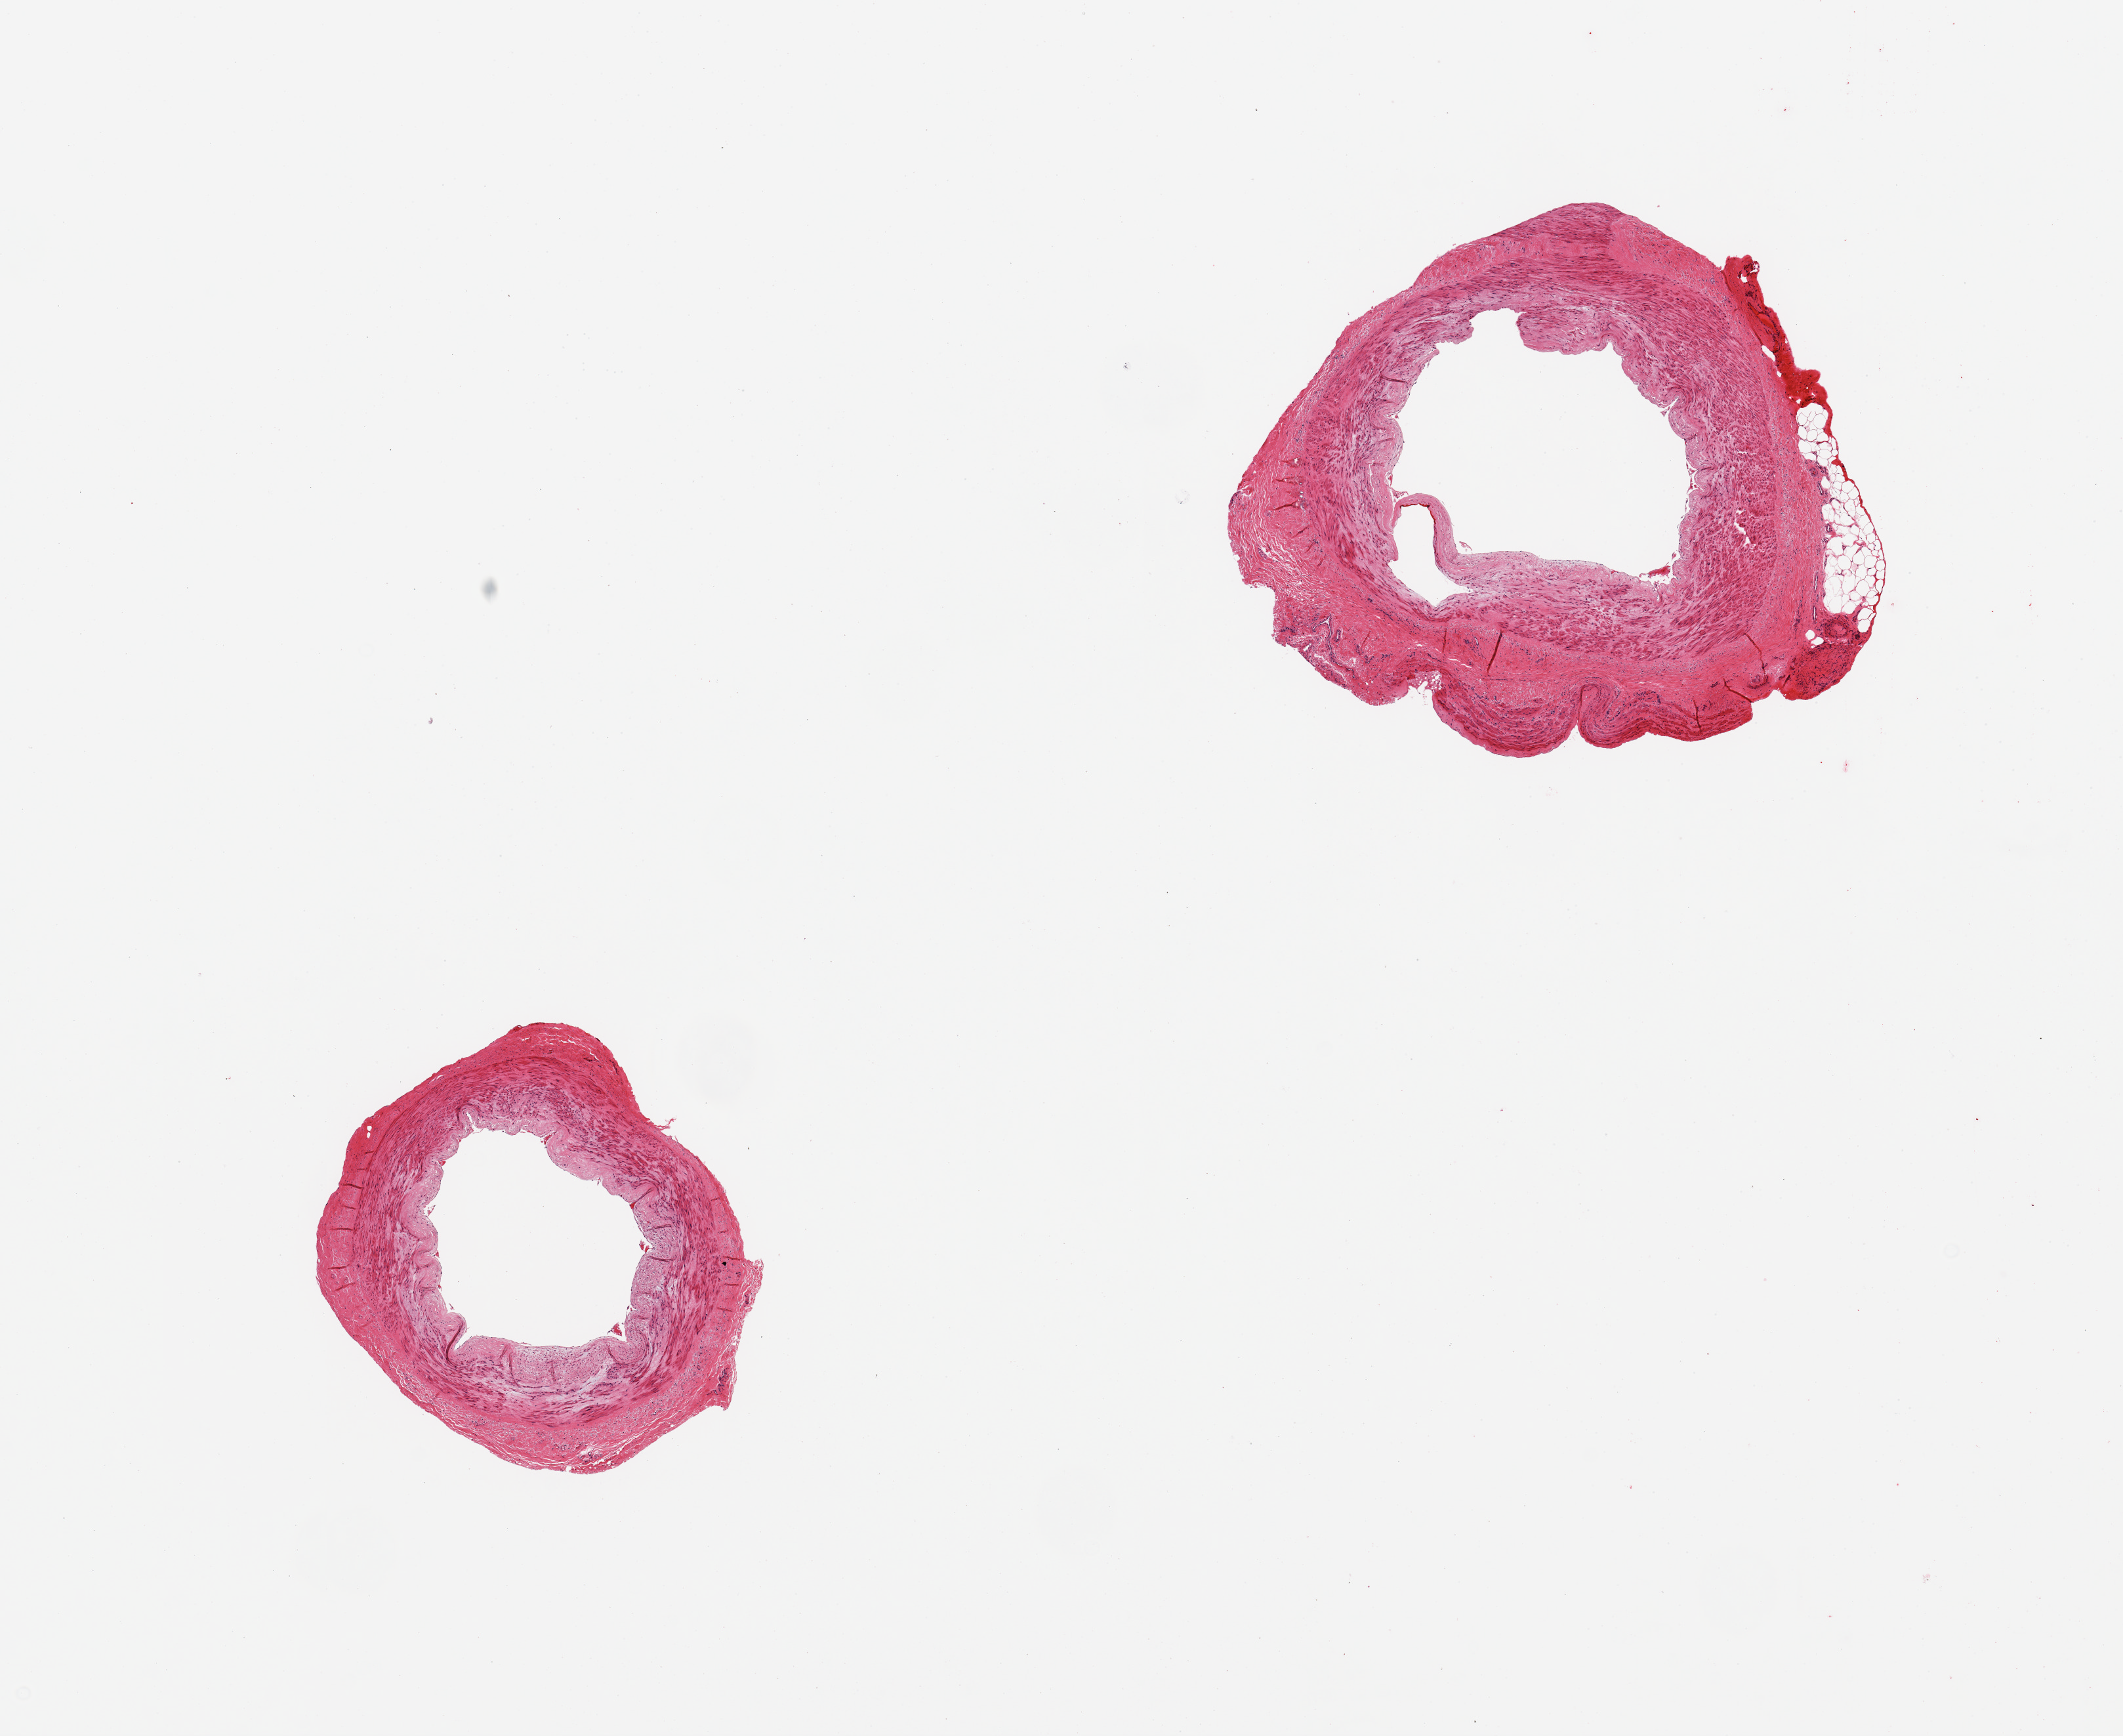
Whole-slide image, H&E stain — a low-resolution overview of the entire scanned area, about 12.8 x 10.5 mm (from a 20x scan); PAXgene-fixed, paraffin-embedded tissue; target tissue: tibial artery; tissue donor sample. Donor sex: male.
• reviewer comment on this tissue sample: 2 pieces, no significant atherosis, clean sections